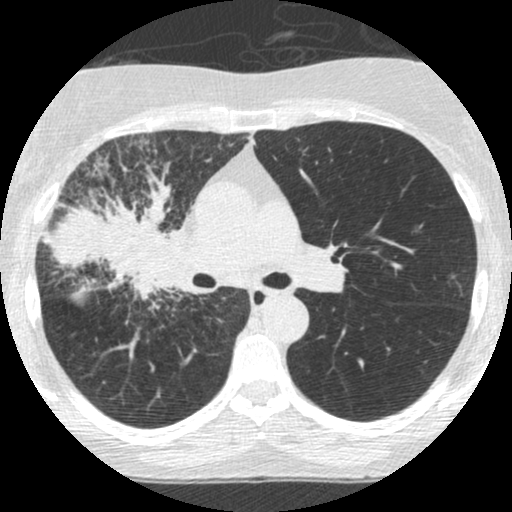
Low-dose screening chest CT, one axial slice; slice 158 of 253 in the series (ordered by position); lung window (W 1500 / L -600 HU); 1.25 mm slice thickness; 512 × 512 image matrix, field of view 294 × 294 mm.
Structures marked on this image (outlined manually by an expert reader):
- lesion 2 (tumor, hilum of right lung): box from (x=42, y=179) to (x=184, y=301) px